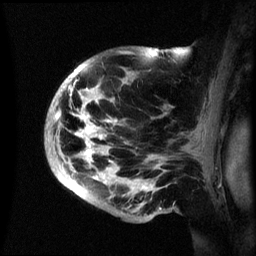
Breast MRI (dynamic contrast-enhanced), one sagittal slice. Dynamic contrast-enhanced series, image 2 of 3 at this slice position (ordered by acquisition). 1.5 T. TE 4.2 ms, TR 8.4 ms. 2.4 mm slice thickness. 256 × 256 image matrix, field of view 230 × 230 mm. Female patient, age 48 years.
Structures marked on this image (semi-automatic segmentation, software-assisted and operator-edited):
- analysis volume of interest (the breast-tissue region the enhancement analysis was run in; not a lesion): box from (x=45, y=48) to (x=191, y=222) px
- tumour enhancement mask (voxels above the 70 % enhancement threshold inside the analysis volume of interest): (x=53, y=49)–(x=157, y=191)